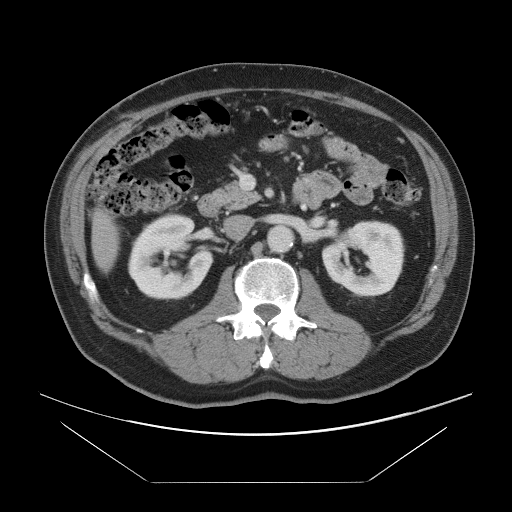
Contrast-enhanced abdominal CT, one axial slice; position 36 of 97 along the scan axis; 120 kVp; intravenous contrast given; soft-tissue window (W 400 / L 40 HU); 512 × 512 image matrix, field of view 442 × 442 mm. Male patient, age 62 years. From the clinical record (not read from this slice): diagnosis: colorectal cancer liver metastases, imaged before liver resection; multiple liver metastases: no; largest metastasis: 7 cm; disease in both lobes: yes.
Annotated regions visible in this slice (manually delineated by an expert):
- liver: bounding box [x1, y1, x2, y2] px = [94, 212, 117, 269]
- planned liver remnant (the part of the liver to remain after resection): [94, 212, 118, 269]